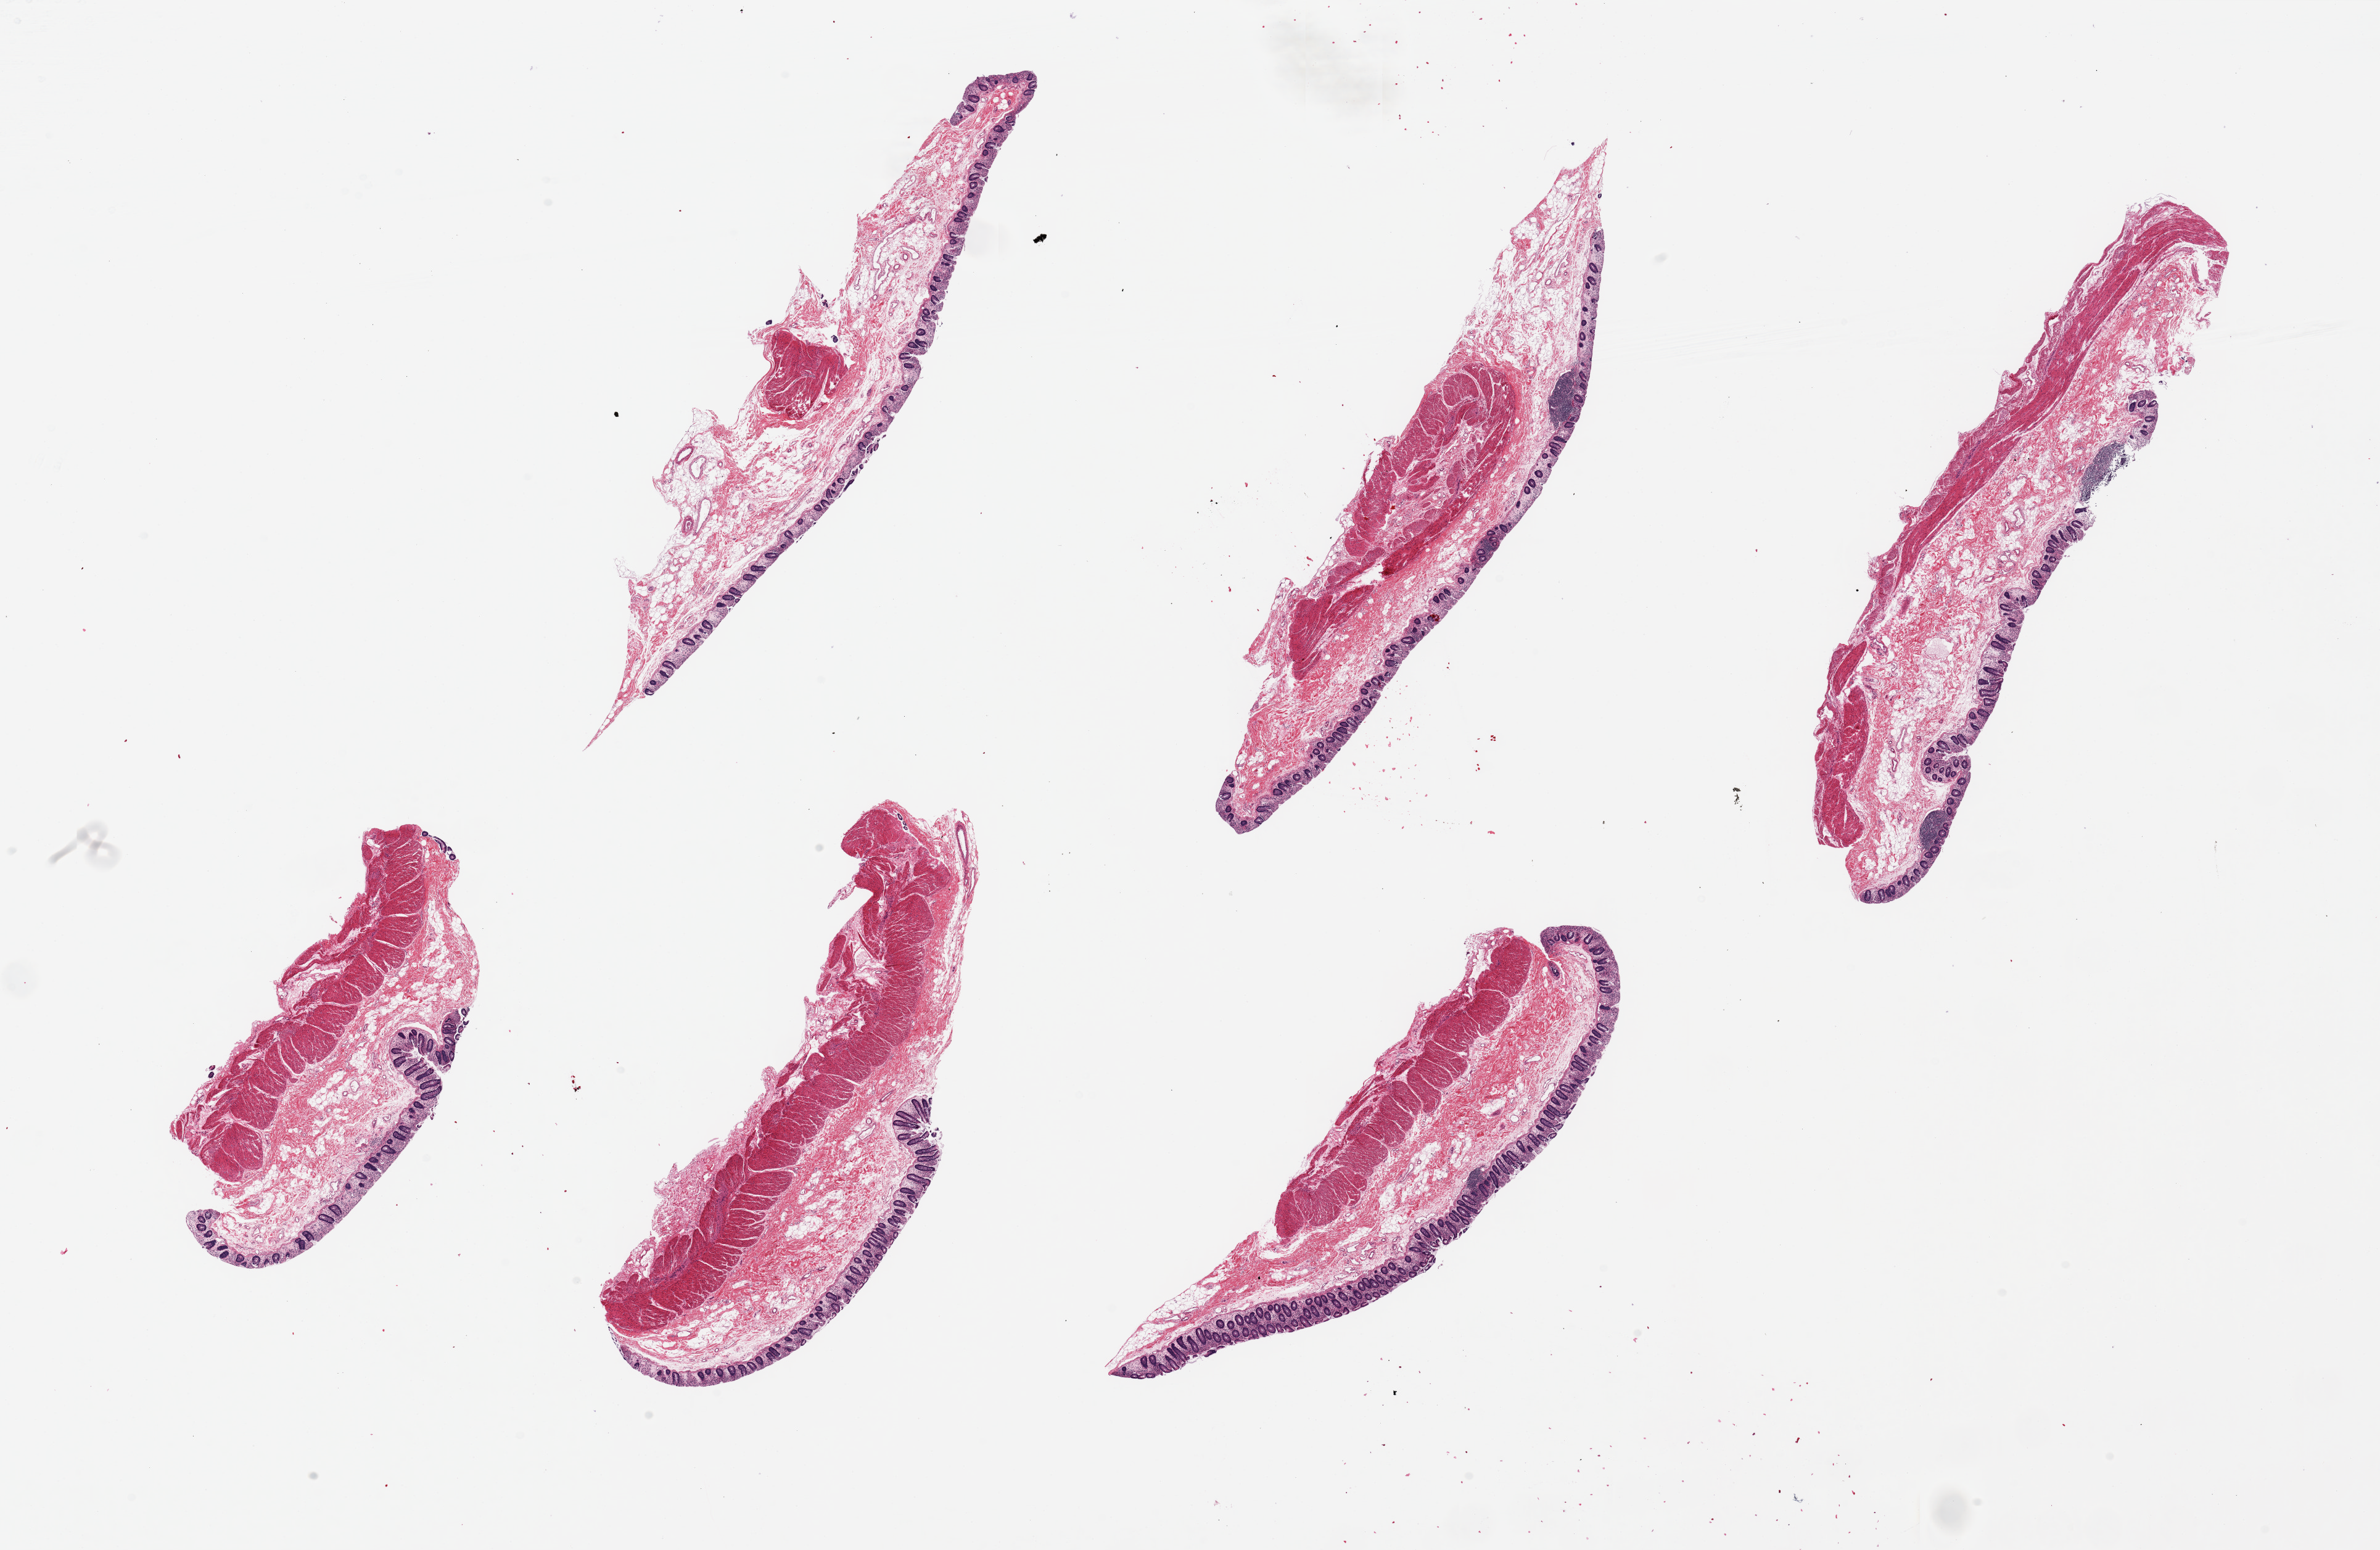
H&E whole-slide image, whole scanned area (about 30.5 x 19.9 mm) shown as a low-resolution overview, PAXgene-fixed, paraffin-embedded tissue, section of transverse colon (target tissue), donor tissue sample. Donor: male.
Reviewer comment on this tissue sample: 6 pieces ~9x2mm. Mucosa partly sloughed, not well preserved.